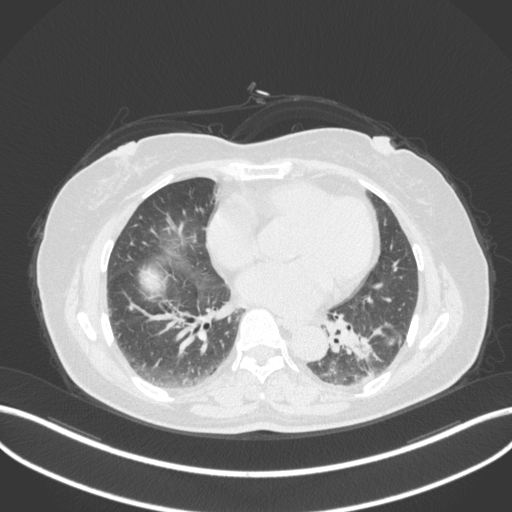
Chest CT, one axial slice. Slice 160 of 307 in the series (ordered by position). 120 kVp. Lung window (W 1500 / L -600 HU). 1 mm slice thickness. 512 × 512 image matrix. Patient: female, 59 years. Case-level facts recorded for this patient, not image findings: clinical TNM (as recorded): T2a N0 M0; histopathological grade: G2-3.
Outlined on this slice (bounding box drawn by a radiologist):
- lung tumour (recorded histology: adenocarcinoma): bounding box [x1, y1, x2, y2] px = [348, 322, 387, 367]